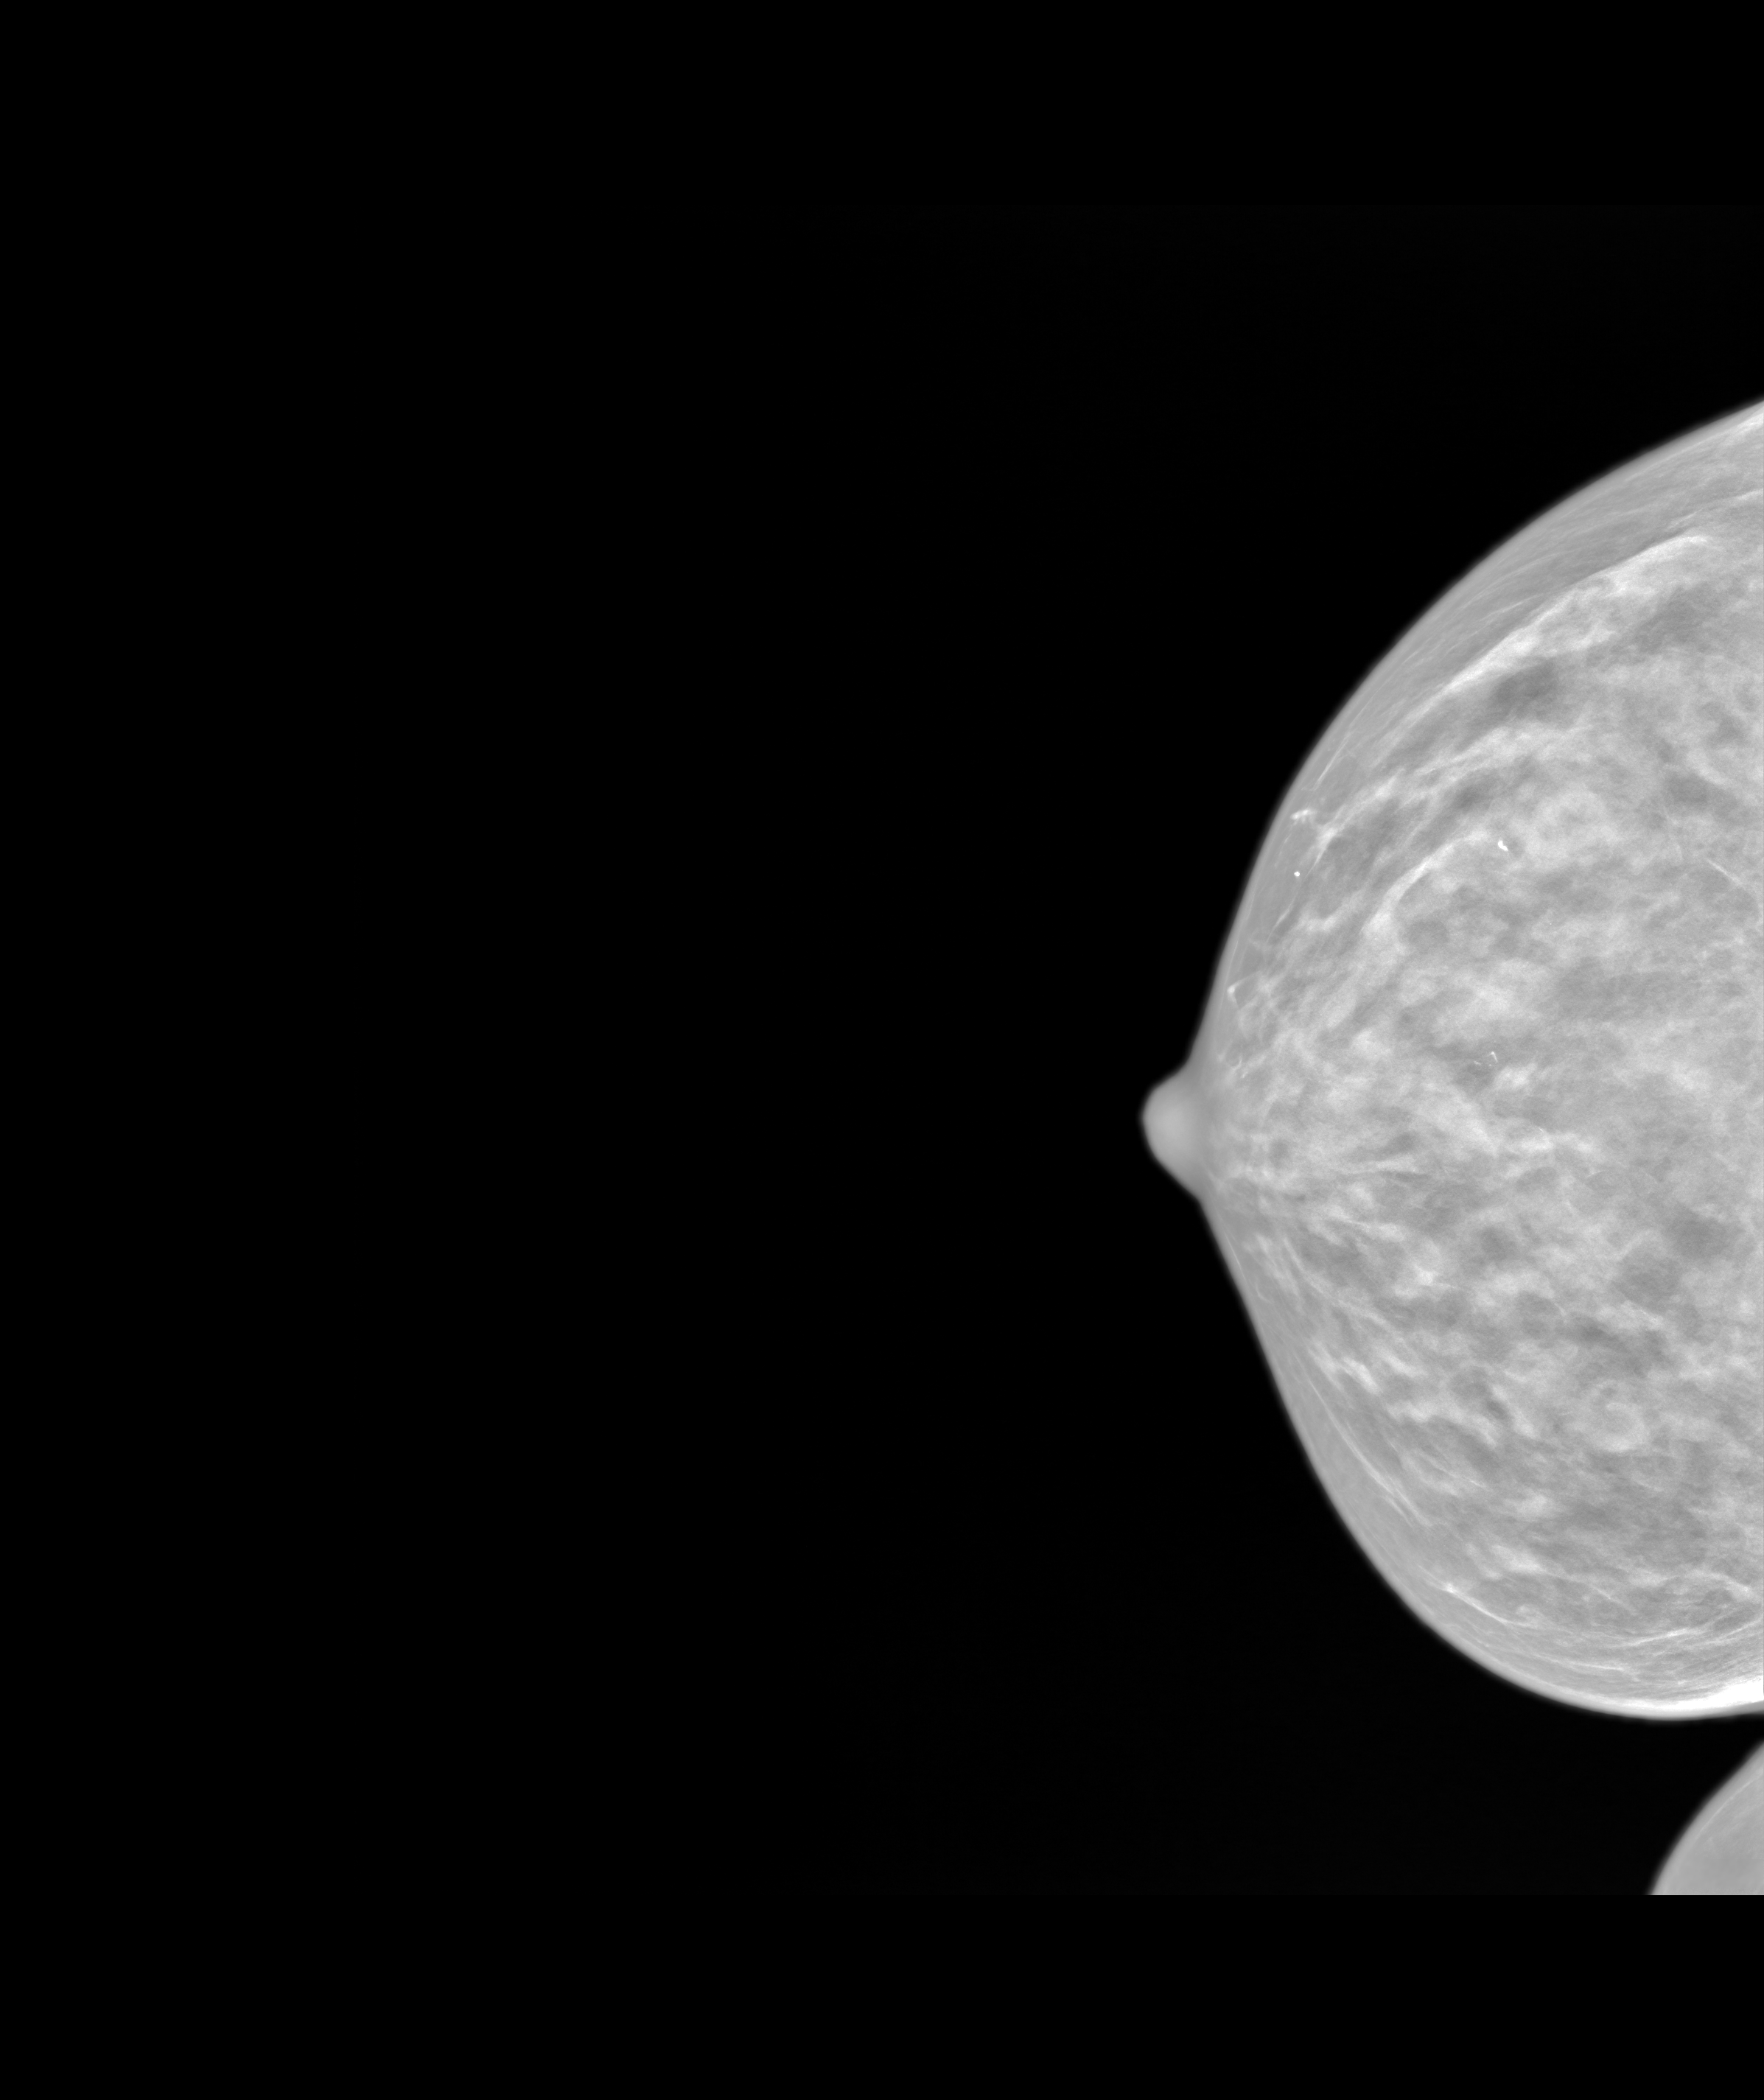
Screening examination. Patient aged 73 years (female).
Image type: synthesized 2-D view from tomosynthesis. Breast: right. Projection: cranio-caudal projection.